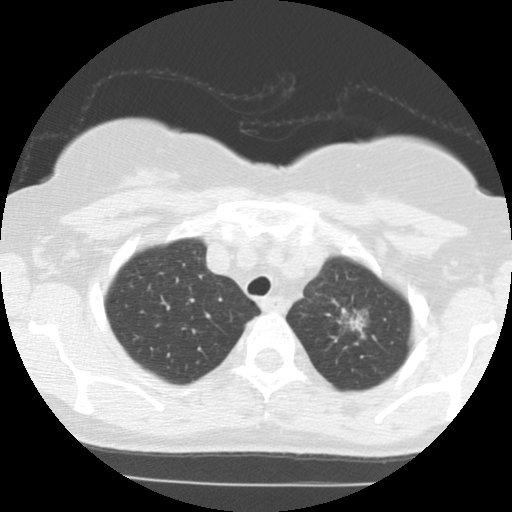
Low-dose screening chest CT, one axial slice. Slice 100 of 123 in the series (ordered by position). Lung window (W 1500 / L -600 HU). 2.5 mm slice thickness. 512 × 512 image matrix, field of view 290 × 290 mm.
Annotated regions visible in this slice (outlined manually by an expert reader):
- lesion 1 (tumor, upper lobe of left lung): bounding box (x1, y1, x2, y2) in pixels: (337, 308, 369, 338)